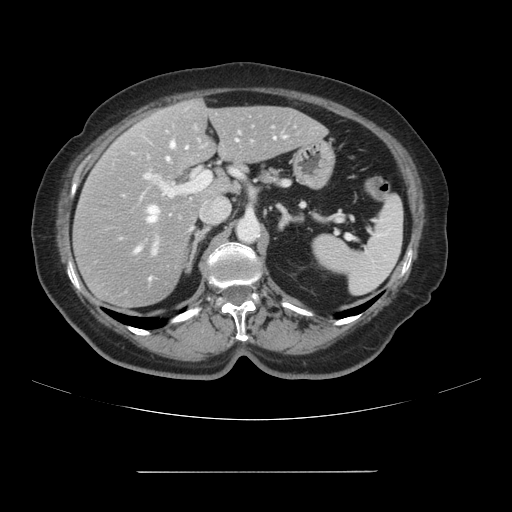
Contrast-enhanced abdominal CT, one axial slice. Position 59 of 111 along the scan axis. Intravenous contrast given. Soft-tissue window (W 400 / L 40 HU). 512 × 512 image matrix, field of view 400 × 400 mm. Female patient, age 74 years. From the clinical record (not read from this slice): diagnosis: colorectal cancer liver metastases, imaged before liver resection; multiple liver metastases: yes; largest metastasis: 1.1 cm; disease in both lobes: yes.
Structures marked on this image (expert manual segmentation):
- hepatic veins: bounding box <137,142,175,251> (left, top, right, bottom; pixels)
- liver: <75,100,325,308>
- planned liver remnant (the part of the liver to remain after resection): <146,100,325,196>
- portal vein (with intrahepatic branches): <122,124,297,254>